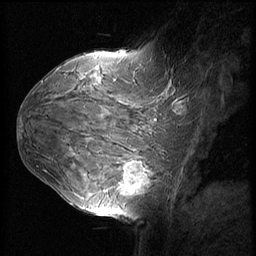
Breast MRI (dynamic contrast-enhanced), one sagittal slice; dynamic contrast-enhanced series, image 2 of 3 at this slice position (ordered by acquisition); 1.5 T; TE 4.2 ms, TR 8.9 ms; 256 × 256 image matrix, field of view 220 × 220 mm. Female patient, age 37 years. From the clinical record (not read from this slice): setting: breast cancer imaged before/during neoadjuvant chemotherapy; receptor status: triple-negative.
Structures marked on this image (semi-automatic segmentation, software-assisted and operator-edited):
- analysis volume of interest (the breast-tissue region the enhancement analysis was run in; not a lesion): box from (x=114, y=153) to (x=159, y=206) px
- tumour enhancement mask (voxels above the 140 % enhancement threshold inside the analysis volume of interest): (x=120, y=162)–(x=149, y=195)